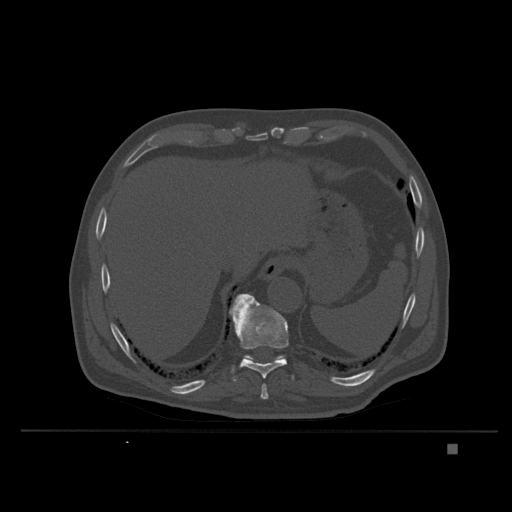
CT including the spine, one axial slice. Position 193 of 435 along the scan axis. Bone window (W 1800 / L 400 HU). 1.5 mm slice thickness. 512 × 512 image matrix, field of view 434 × 434 mm. Patient: male, 73 years. Case-level facts recorded for this patient, not image findings: primary cancer: skin.
Structures marked on this image (semi-automatic segmentation, software-assisted and operator-edited):
- T10 vertebra: bounding box <231,303,294,382> (left, top, right, bottom; pixels)
- T11 vertebra: <229,294,286,362>
- T9 vertebra: <260,384,269,401>